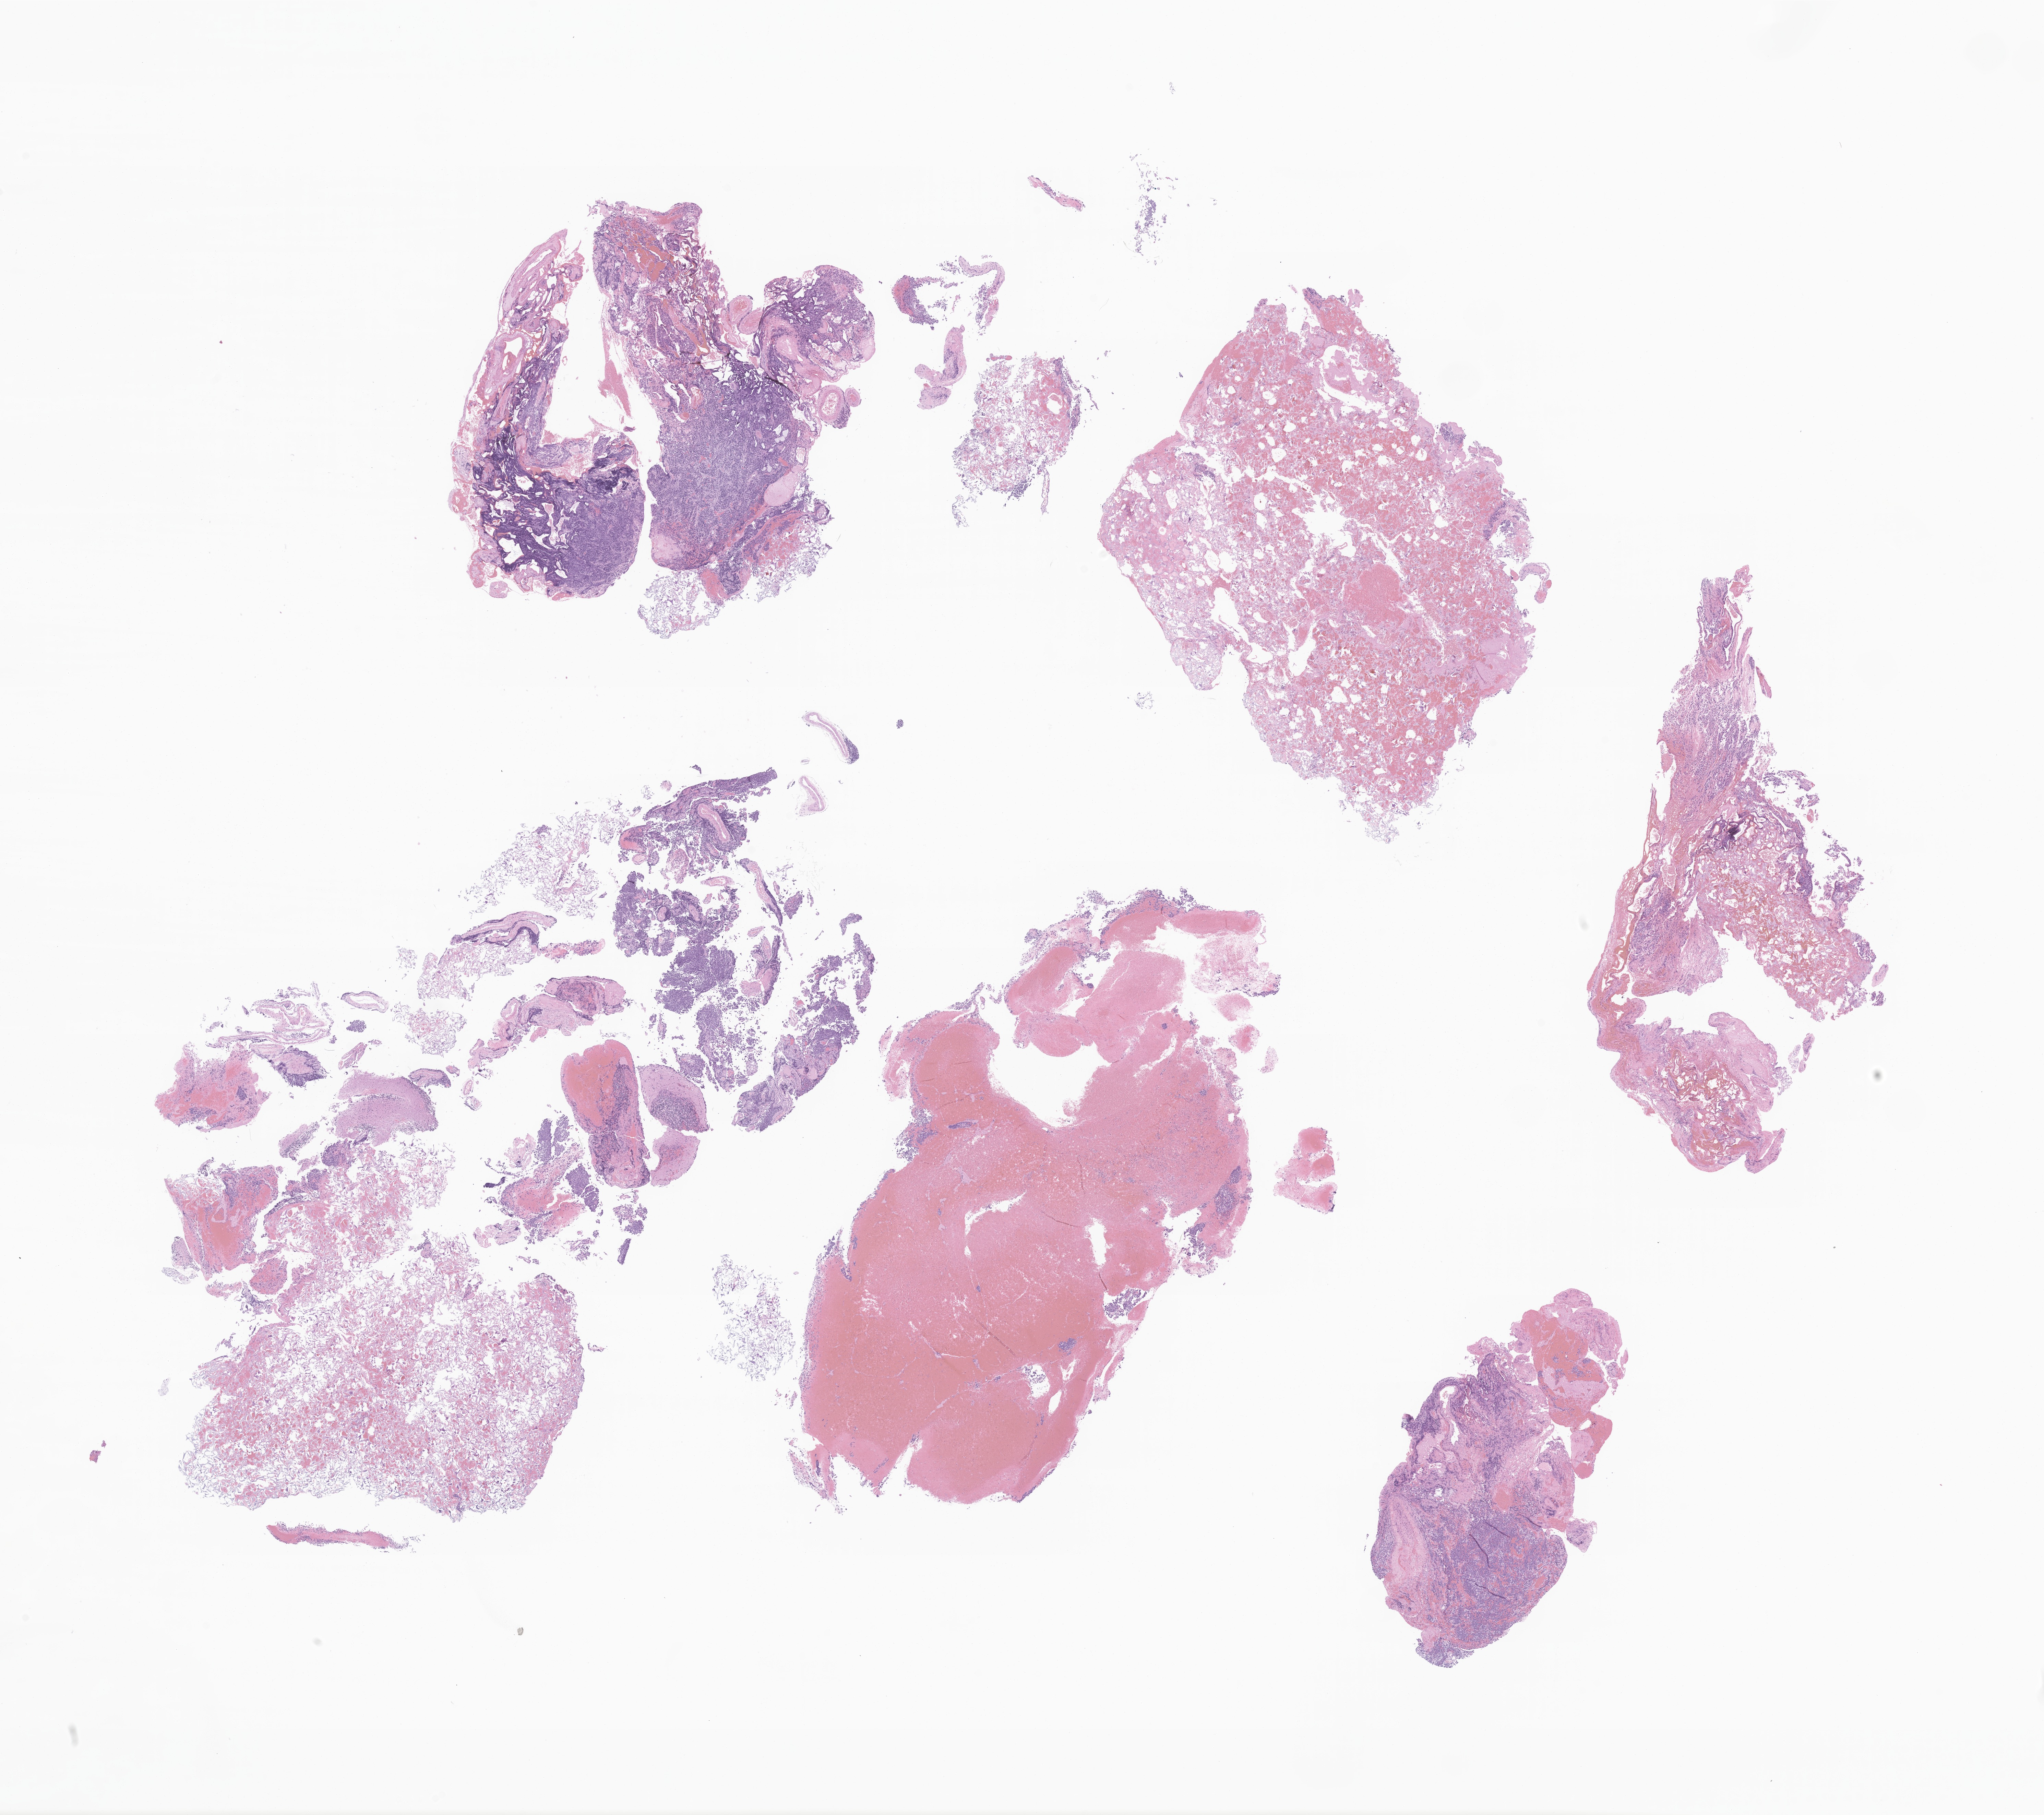
Digitized haematoxylin and eosin-stained section of tumor tissue from the cerebellum — low-resolution overview of the scanned area, about 25.1 x 22.3 mm, formalin-fixed, paraffin-embedded (FFPE) tissue. Male patient, age 176 months (14 years 8 months).
- diagnosis: Medulloblastoma, NOS